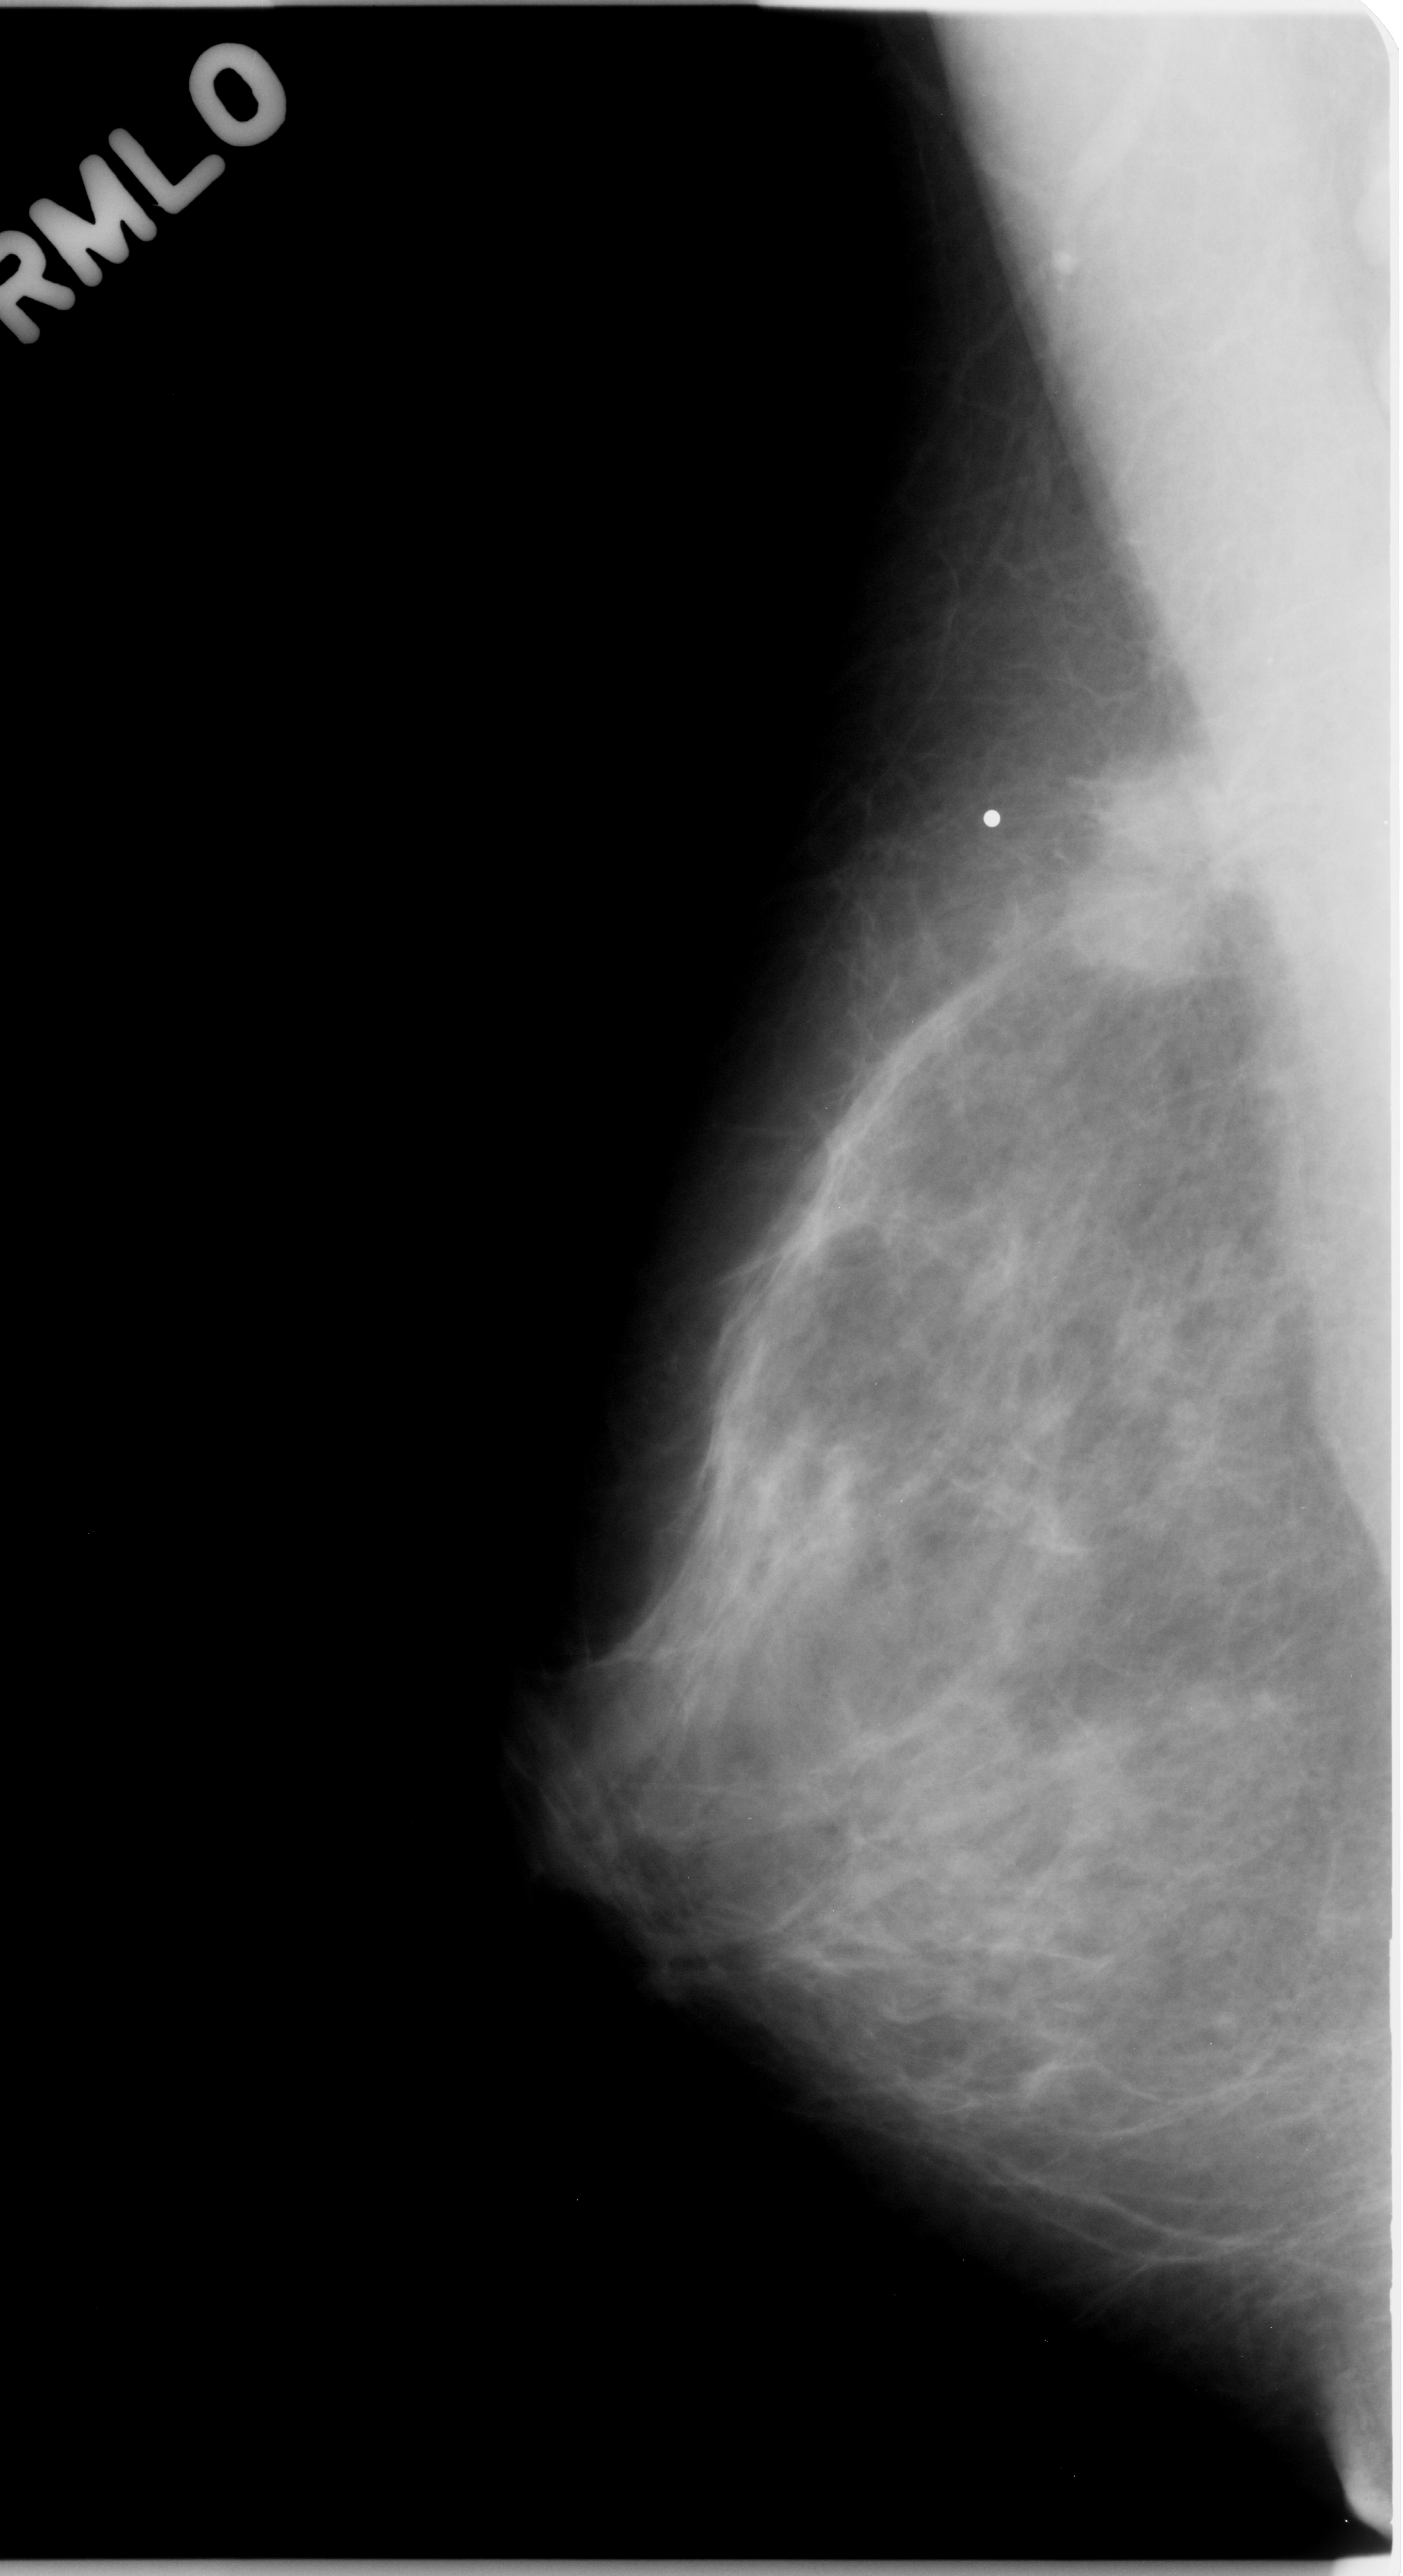
Mammogram (digitized film). Right breast. Mediolateral oblique (MLO) view. BI-RADS breast density category 2 (scale 1–4). 1403 × 2576 image matrix.
Marked abnormalities (boxes around the expert regions of interest):
- mass, shape irregular, margins spiculated; BI-RADS assessment category 5; subtlety rating 5 on a 1 (subtle) to 5 (obvious) scale; pathology (as recorded): malignant: box from (x=1077, y=735) to (x=1269, y=931) px